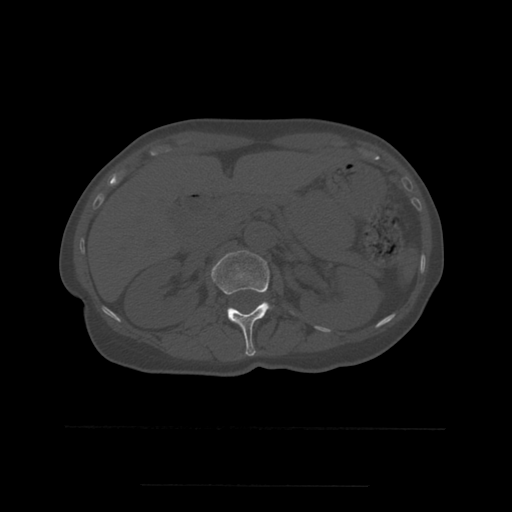
CT including the spine, one axial slice. Position 231 of 544 along the scan axis. Bone window (W 1800 / L 400 HU). 1.25 mm slice thickness. 512 × 512 image matrix. Patient age 58 years. Case-level facts recorded for this patient, not image findings: primary cancer: lung.
Annotated regions visible in this slice (semi-automatically segmented with operator editing):
- L1 vertebra: bounding box (x1, y1, x2, y2) in pixels: (211, 251, 294, 357)